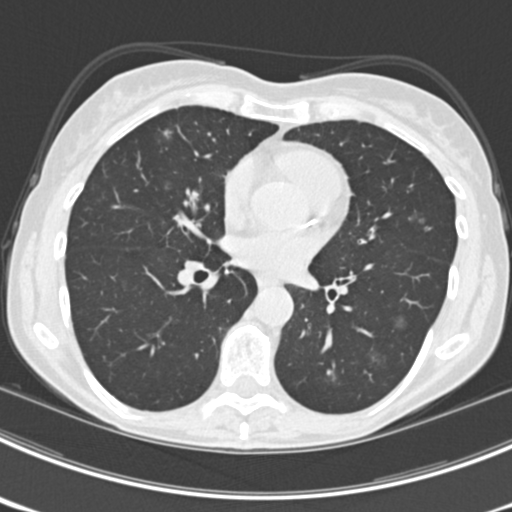
Axial slice from a low-dose chest CT screening exam, third screening round (two years after baseline), lung window (W 1500 / L -600 HU), 512 × 512 image matrix, field of view 302 × 302 mm. Female, age 63 years at enrolment. Current smoker at enrolment.
Expert-annotated lung lesion, bounding box [x1, y1, x2, y2] px = [405, 200, 445, 236]. The screening reader recorded 9 non-calcified nodules or masses ≥4 mm on this exam; which of them this box marks is not recorded. Official screen result: positive, other. Participant outcome: lung cancer diagnosed 15 days after this screen — bronchiolo-alveolar adenocarcinoma, NOS, right upper lobe, right middle lobe, right lower lobe, left upper lobe, left lower lobe, moderately differentiated (G2), stage IV (AJCC 6th edition).